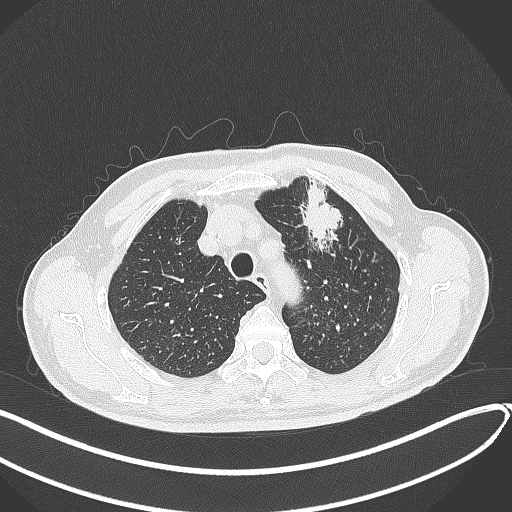
Chest CT, one axial slice; position 339 of 459 along the scan axis; reconstruction kernel B70f; lung window (W 1500 / L -600 HU); 1 mm slice thickness; 512 × 512 image matrix, field of view 400 × 400 mm. Male patient, age 74 years. Case-level facts recorded for this patient, not image findings: clinical TNM (as recorded): T2b N0 M1c.
Structures marked on this image (bounding box drawn by a radiologist):
- lung tumour (recorded histology: adenocarcinoma): bounding box [x1, y1, x2, y2] px = [298, 180, 348, 250]